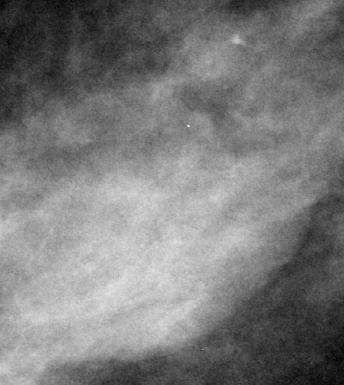
Cropped region of a digitized screen-film mammogram centred on a radiologist-marked abnormality; right breast; CC view; BI-RADS breast density category 2 (scale 1–4).
- Mass, shape oval, margins obscured; BI-RADS assessment category 3; pathology result (as recorded, not read from the image): benign.